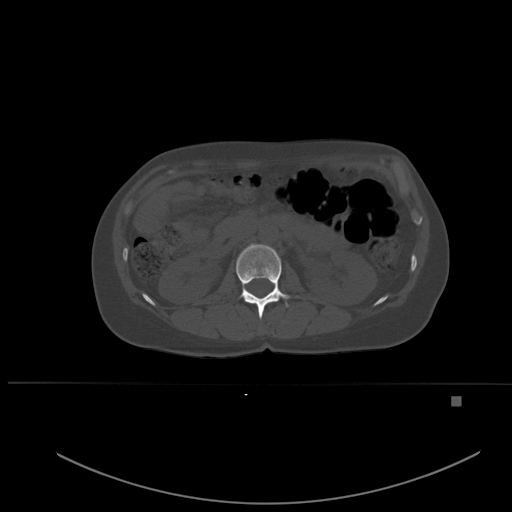
CT including the spine, one axial slice. Slice 232 of 651 in the series (ordered by position). Bone window (W 1800 / L 400 HU). 1.5 mm slice thickness. 512 × 512 image matrix, field of view 443 × 443 mm. Female patient, age 49 years. Case-level facts recorded for this patient, not image findings: primary cancer: breast; vertebrae with lytic lesions (as recorded): L3, T12, L4.
Outlined on this slice (semi-automatic segmentation, software-assisted and operator-edited):
- L1 vertebra: bounding box (x1, y1, x2, y2) in pixels: (236, 244, 290, 319)